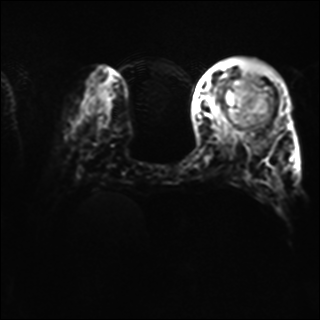
Breast MRI, one axial slice. Slice 15 of 40 in the series (ordered by position). Diffusion-weighted series; image 2 of 4 stored at this slice position (different b-values; order by instance number). 1.5 T. 320 × 320 image matrix, field of view 320 × 320 mm. Female patient.
Annotated regions visible in this slice (outlined manually by an expert reader):
- tumour on diffusion-weighted imaging: box from (x=225, y=80) to (x=270, y=127) px